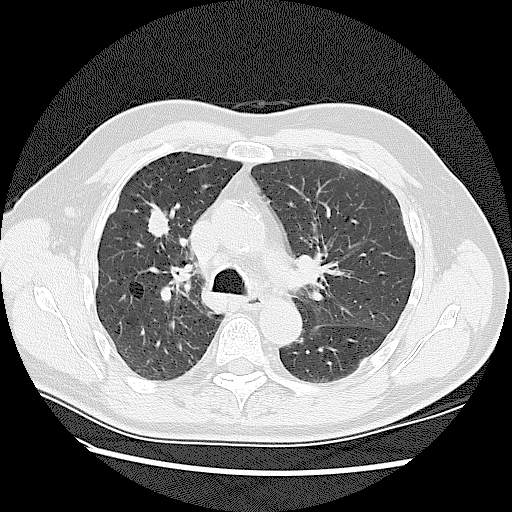
Chest CT (low-dose screening protocol), one axial image; baseline screening round; lung window (W 1500 / L -600 HU); 2.5 mm slice thickness; 120 kVp; slice 45 of 128 in the series; 512 × 512 image matrix. Male participant, aged 72 years at enrolment.
• Lesion marked by an expert reader, box from (x=133, y=202) to (x=181, y=240) px.
• The screening reader recorded 2 non-calcified nodules or masses ≥4 mm on this exam (right upper lobe, right upper lobe); which of them this box marks is not recorded.
• Later outcome: lung cancer diagnosed 42 days after this screen — adenocarcinoma, NOS, right upper lobe, stage IV (AJCC 6th edition), 45 mm at pathology.